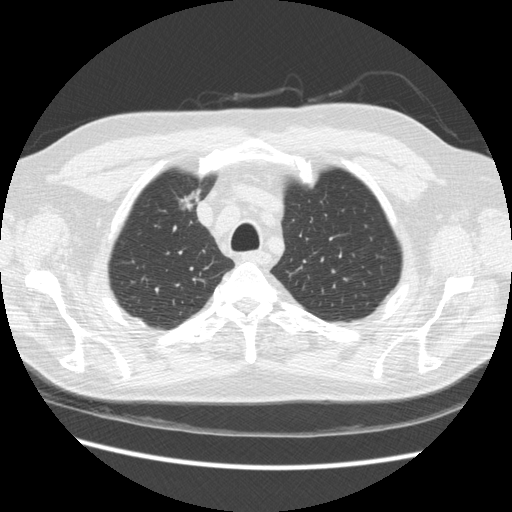
Low-dose screening chest CT, one axial slice. Position 188 of 234 along the scan axis. 120 kVp. Lung window (W 1500 / L -600 HU). 2.5 mm slice thickness. 512 × 512 image matrix.
Annotated regions visible in this slice (manually delineated by an expert):
- lesion 1 (tumor, upper lobe of right lung): bounding box (x1, y1, x2, y2) in pixels: (179, 188, 201, 211)